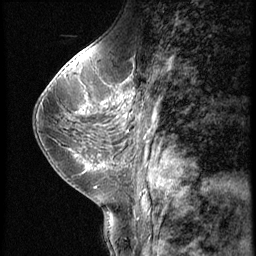
Breast MRI (dynamic contrast-enhanced), one sagittal slice. Position 28 of 56 along the scan axis. Dynamic contrast-enhanced series, image 2 of 3 at this slice position (ordered by acquisition). 1.5 T. TE 4.2 ms, TR 9 ms. 256 × 256 image matrix, field of view 180 × 180 mm. Patient: female, 38 years. From the clinical record (not read from this slice): setting: breast cancer imaged before/during neoadjuvant chemotherapy; receptor status: triple-negative.
Annotated regions visible in this slice (semi-automatic segmentation, software-assisted and operator-edited):
- analysis volume of interest (the breast-tissue region the enhancement analysis was run in; not a lesion): bounding box <107,95,179,149> (left, top, right, bottom; pixels)
- tumour enhancement mask (voxels above the 140 % enhancement threshold inside the analysis volume of interest): <113,98,126,106>